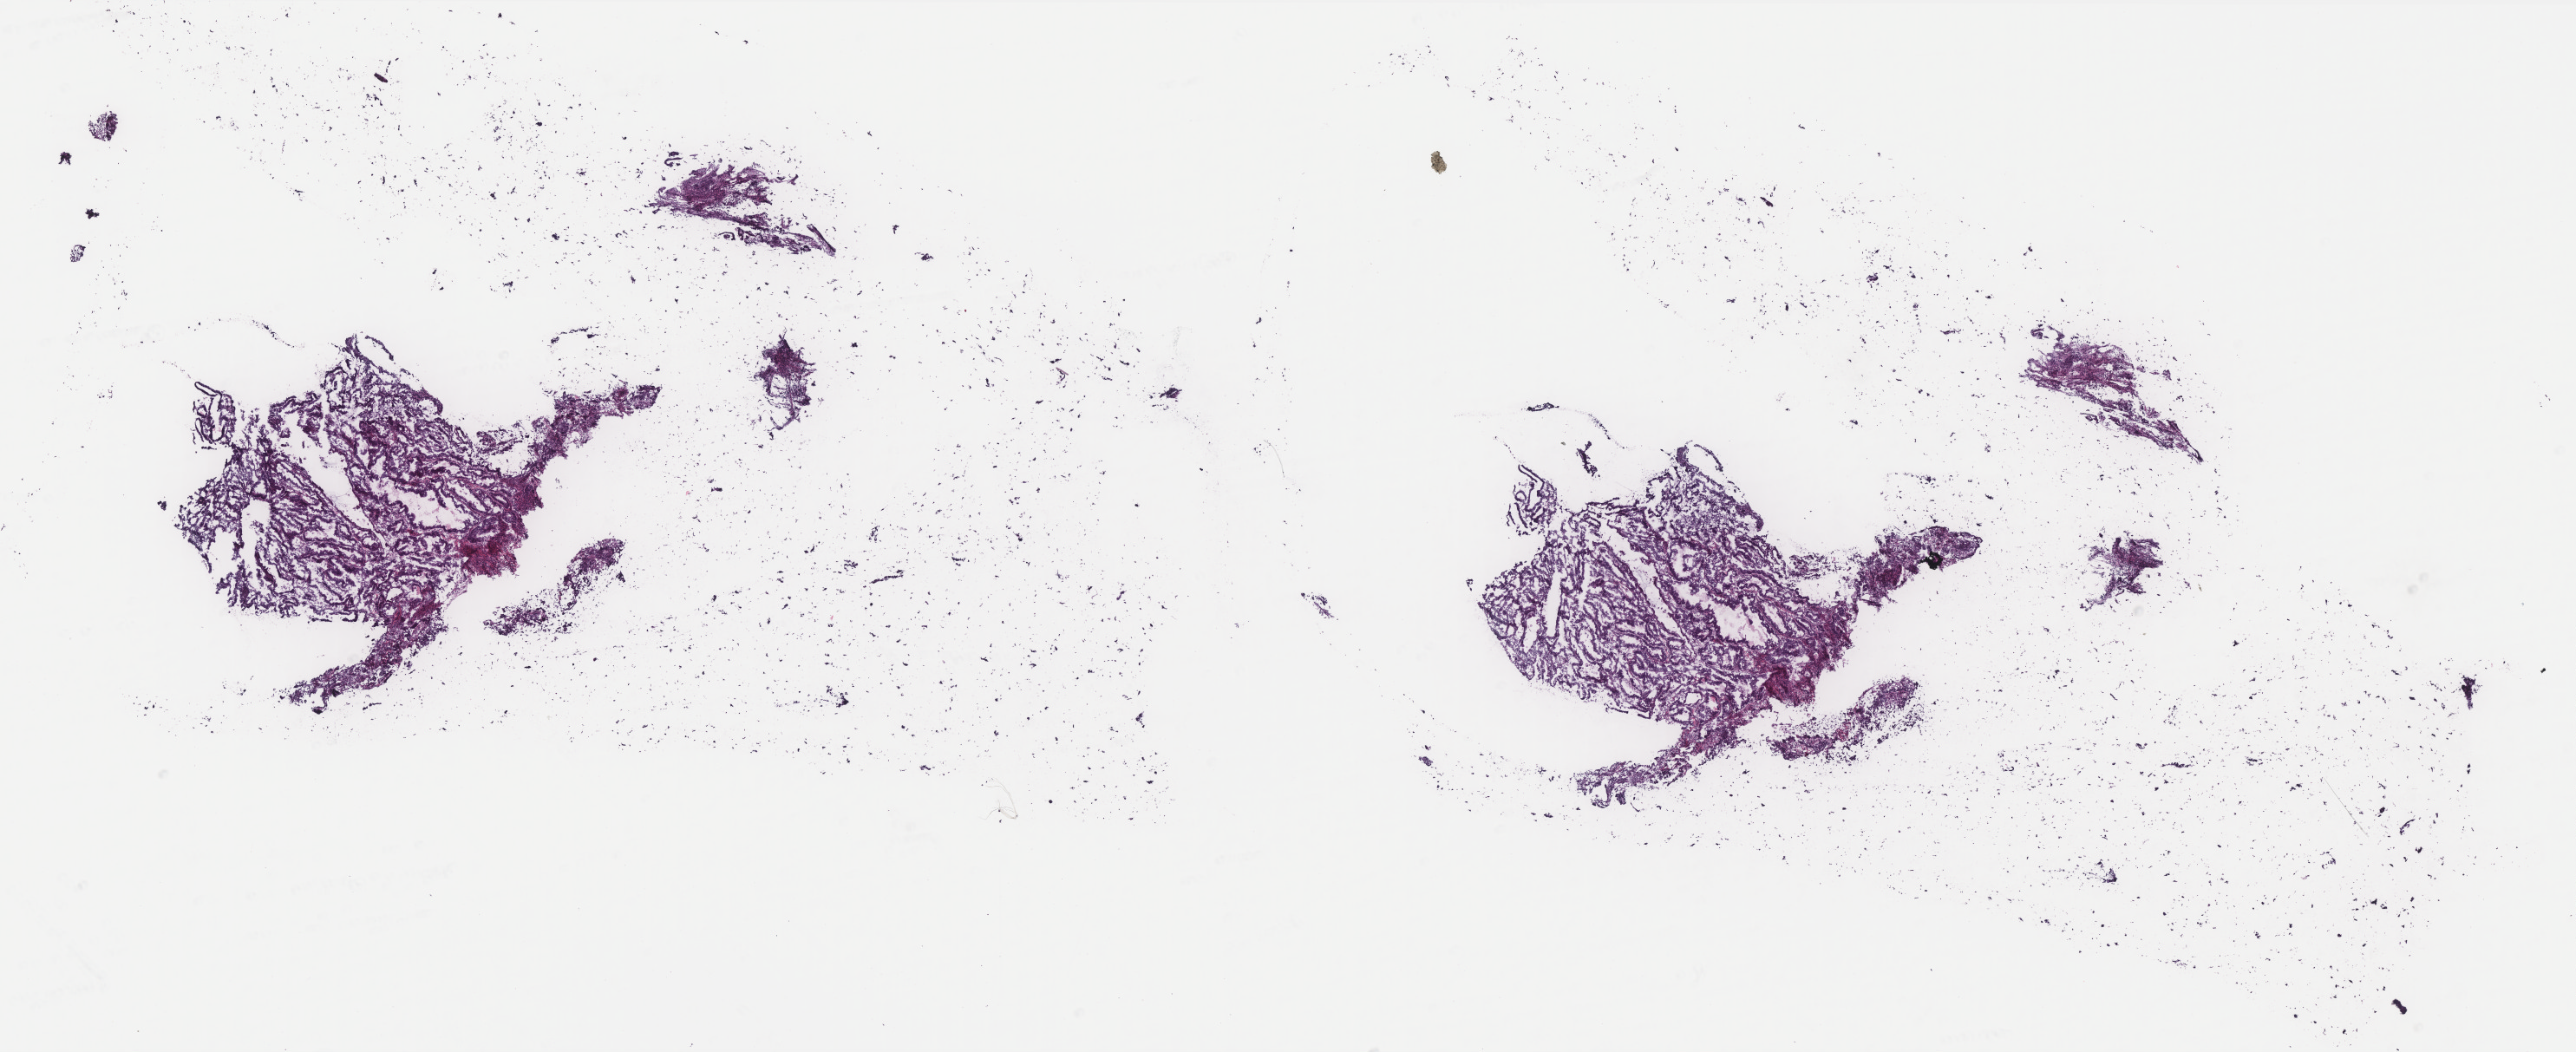
H&E-stained whole-slide image — a low-resolution overview of the entire scanned area, about 23.8 x 9.7 mm (slide scanned at 40x). Frozen section. Primary tumour sample from the uterus. Female, age 57 years at initial diagnosis. Histologic grade: G1 (well differentiated).
Pathologic diagnosis: Endometrioid adenocarcinoma, NOS (endometrium). FIGO stage: IIIA.